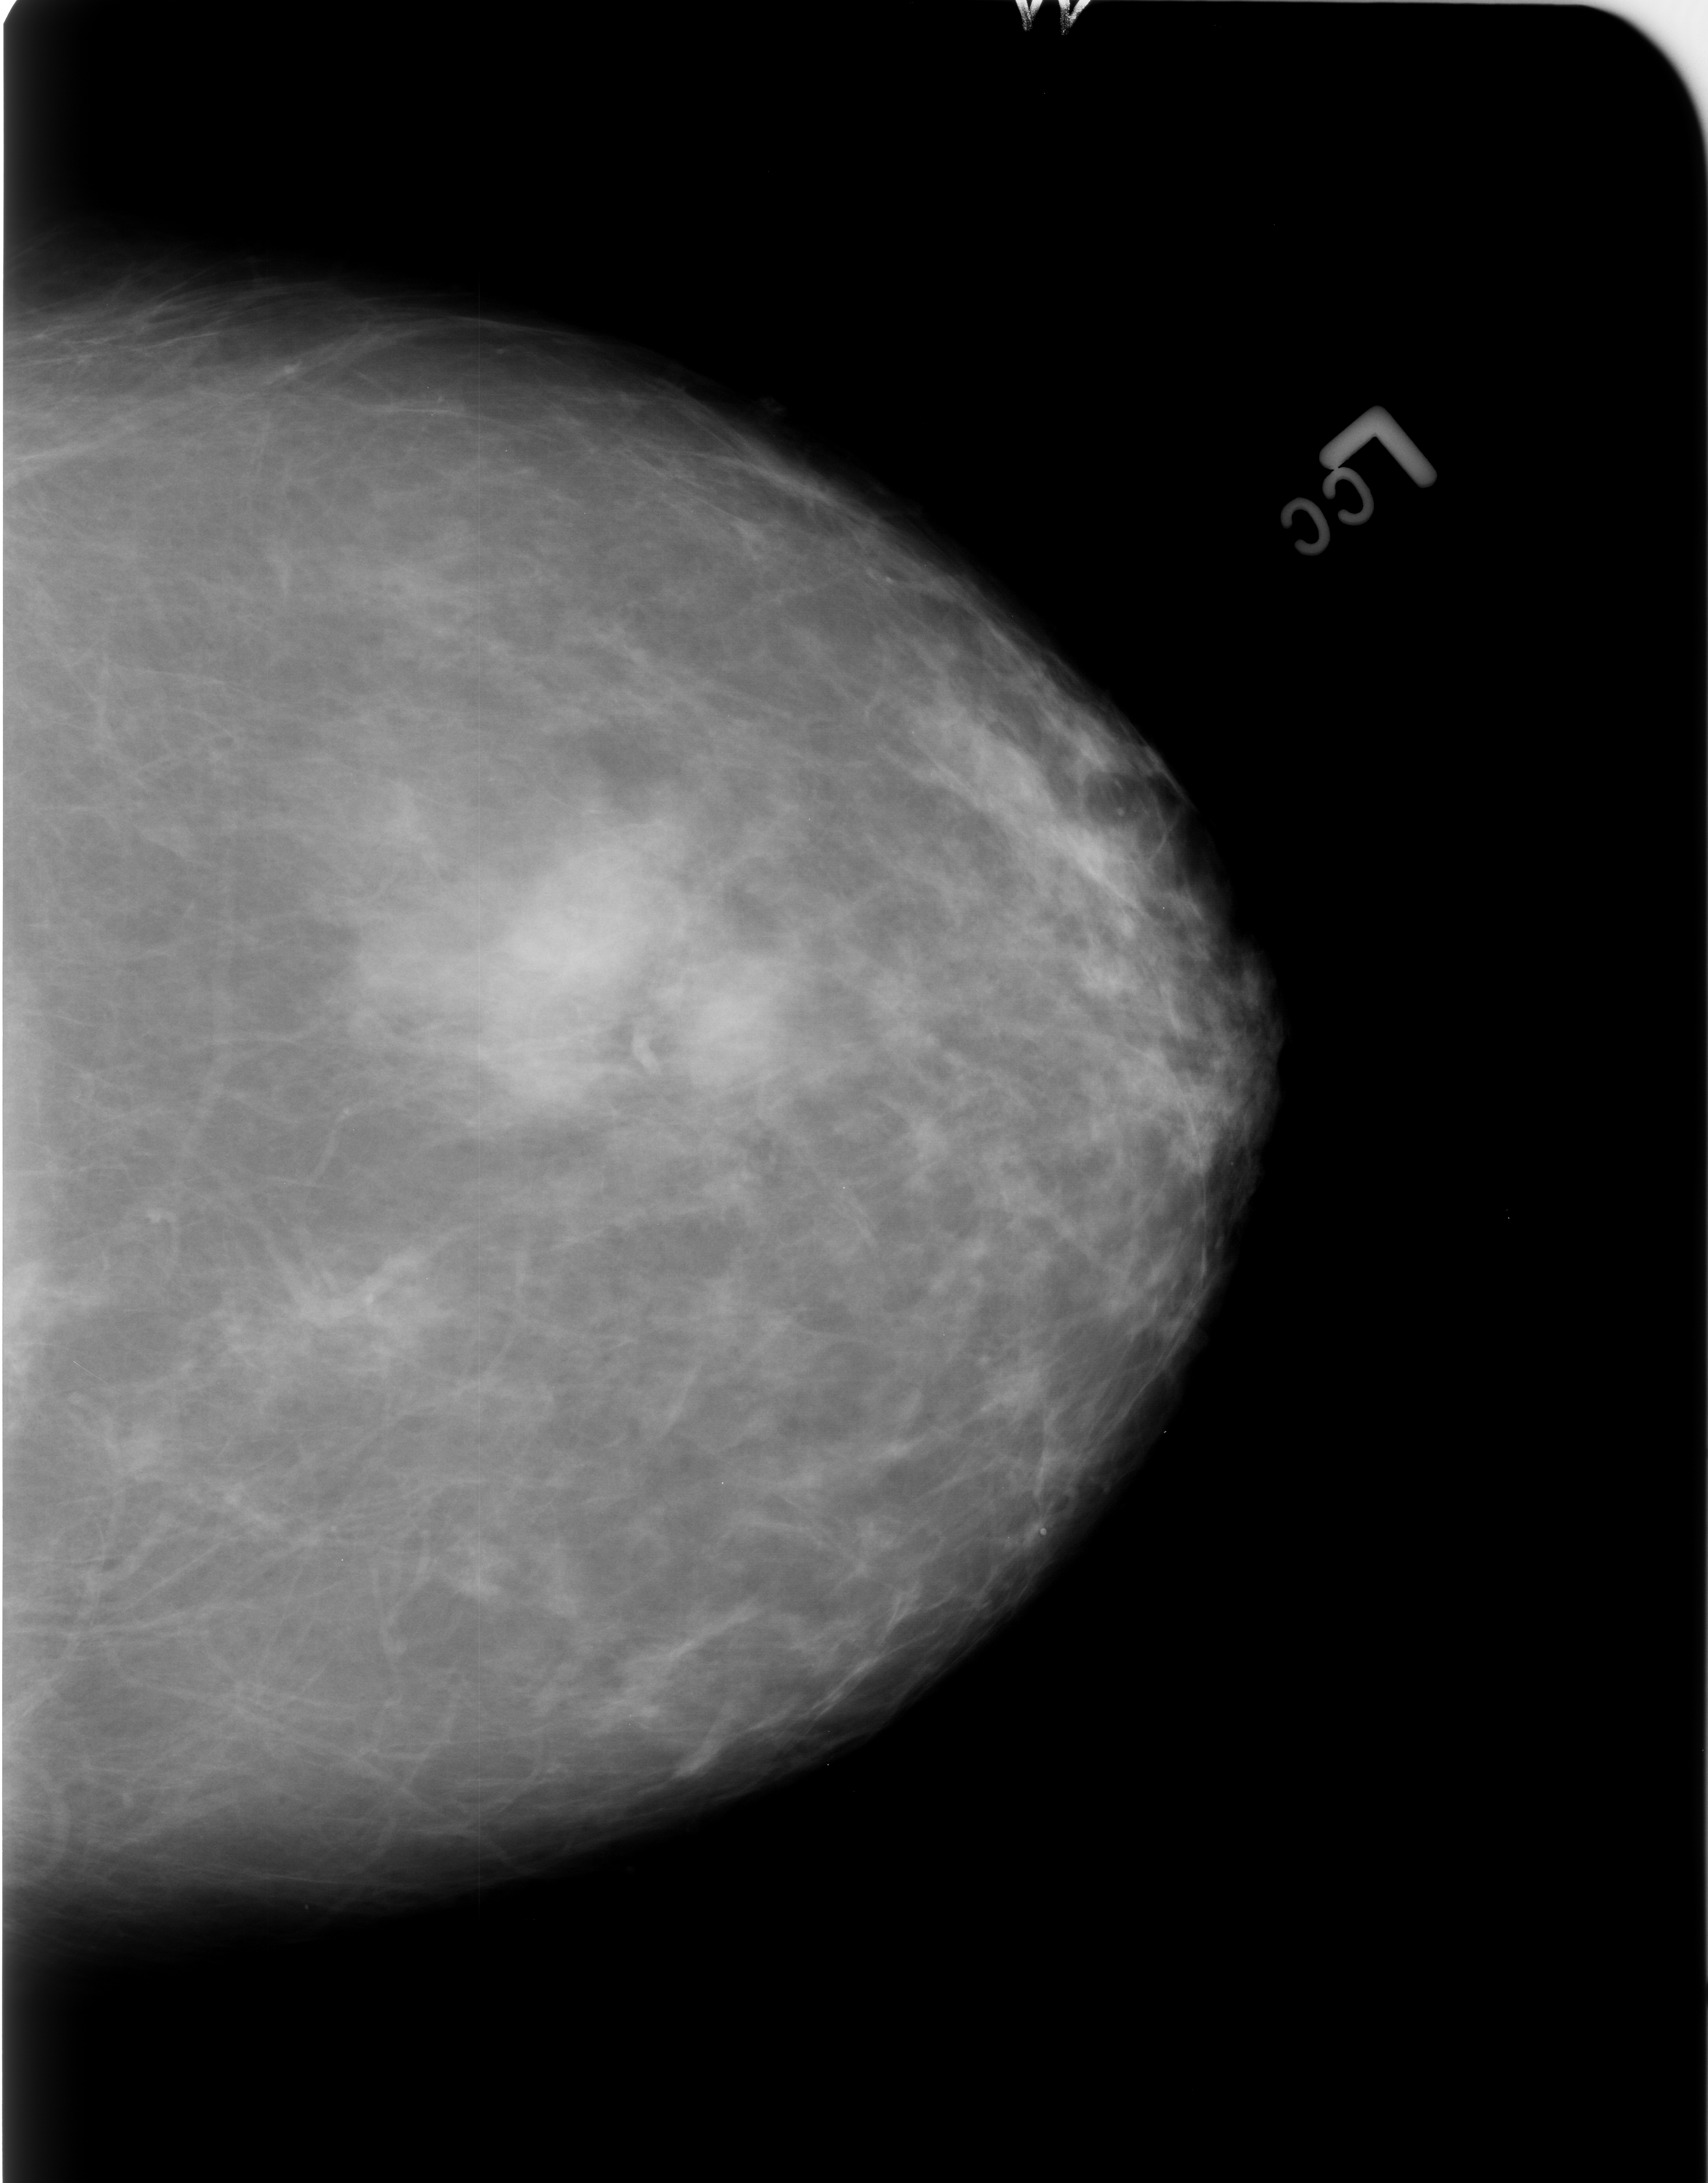
Mammogram (digitized film). Left breast. CC view. Breast composition: scattered fibroglandular densities (BI-RADS density category 2 of 4). 1708 × 2183 image matrix.
Expert-marked regions of interest on this film, with their recorded descriptors:
- calcifications, morphology round and regular; BI-RADS assessment category 2; outcome (as recorded, no biopsy): benign without callback (not worked up further): box from (x=1035, y=1516) to (x=1053, y=1545) px